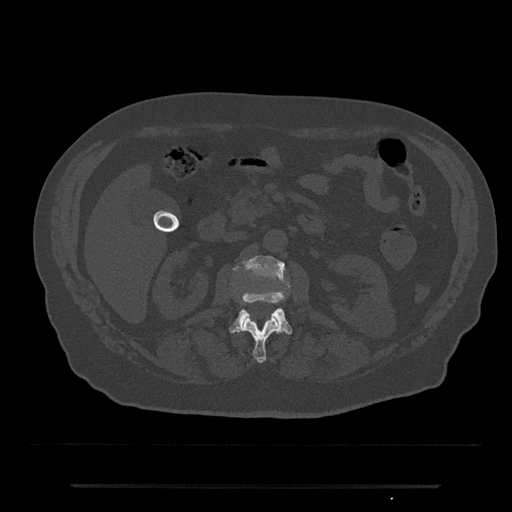
CT including the spine, one axial slice. Bone window (W 1800 / L 400 HU). 0.5 mm slice thickness. 512 × 512 image matrix, field of view 434 × 434 mm. Patient: male, 80 years. Case-level facts recorded for this patient, not image findings: primary cancer: prostate; vertebrae with lytic lesions (as recorded): L1, T11.
Annotated regions visible in this slice (semi-automatic segmentation, software-assisted and operator-edited):
- L1 vertebra: bounding box [x1, y1, x2, y2] px = [243, 317, 280, 363]
- L2 vertebra: [229, 256, 292, 335]